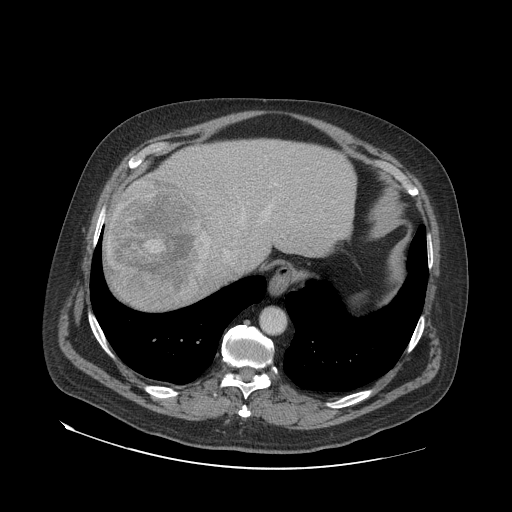
Contrast-enhanced abdominal CT (liver protocol), one axial slice; reconstruction kernel STANDARD; 140 kVp; soft-tissue window (W 400 / L 40 HU); 2.5 mm slice thickness; 512 × 512 image matrix, field of view 480 × 480 mm. Case-level facts recorded for this patient, not image findings: diagnosis: hepatocellular carcinoma (patient treated with transarterial chemoembolisation; whether this scan precedes or follows treatment is not stated here); TNM stage (as recorded): Stage-IVA; Child-Pugh class: A.
Annotated regions visible in this slice (semi-automatically segmented with operator editing):
- abdominal aorta: bounding box [x1, y1, x2, y2] px = [261, 308, 285, 333]
- liver parenchyma outside the tumour (the mass and vessels are separate outlines, so this box may not span the whole liver): [104, 140, 356, 310]
- mass: [108, 177, 210, 307]
- liver vessels: [266, 184, 277, 215]